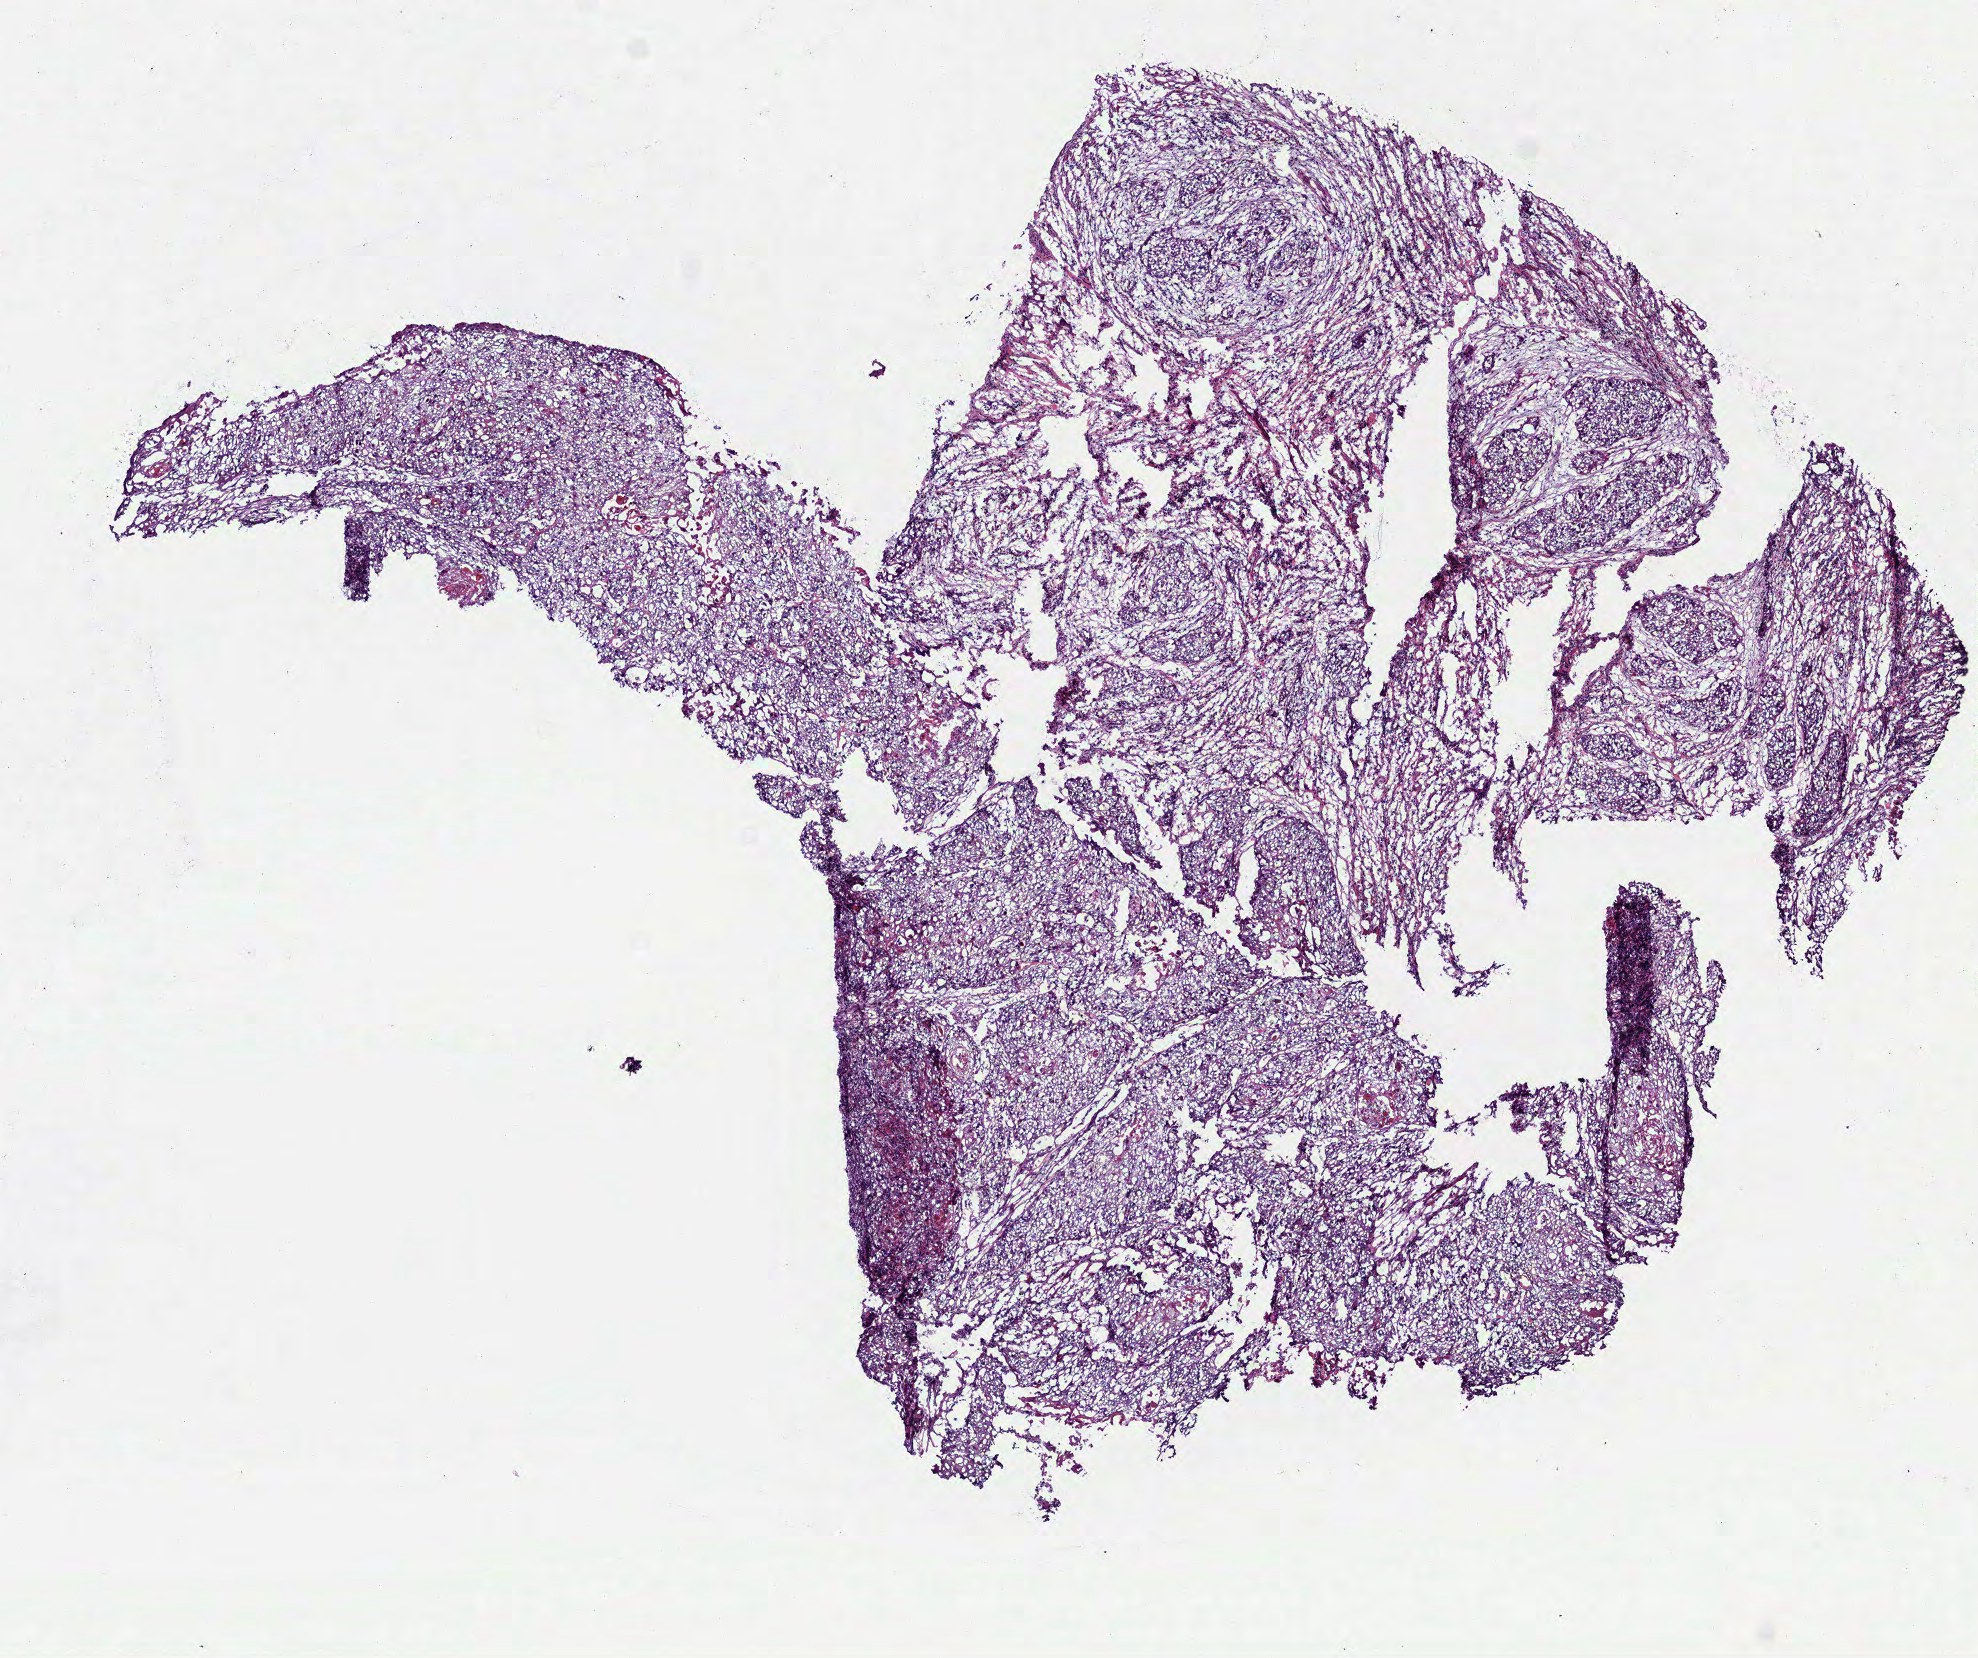
Whole-slide histology image, H&E-stained — shown as a low-resolution overview of the whole scanned area (about 8.0 x 6.7 mm, slide scanned at 40x), frozen section from the top of the tissue portion, sample: primary tumour, head and neck. Patient: female, age at initial diagnosis 50 years. Pathologist review of this section (percent, as recorded): tumour cells 85%, tumour nuclei 85%.
Diagnosis: Squamous cell carcinoma, NOS (tongue, NOS).